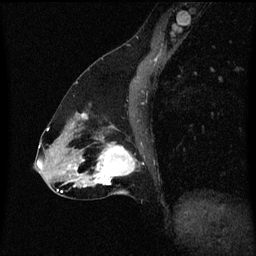
Breast MRI (dynamic contrast-enhanced), one sagittal slice; position 29 of 60 along the scan axis; dynamic contrast-enhanced series, image 2 of 3 at this slice position (ordered by acquisition); 1.5 T; TE 4.2 ms, TR 8.4 ms; 2 mm slice thickness; 256 × 256 image matrix, field of view 200 × 200 mm. Patient: female, 47 years.
Outlined on this slice (semi-automatically segmented with operator editing):
- analysis volume of interest (the breast-tissue region the enhancement analysis was run in; not a lesion): bounding box <85,136,135,197> (left, top, right, bottom; pixels)
- tumour enhancement mask (voxels above the 70 % enhancement threshold inside the analysis volume of interest): <85,144,135,187>